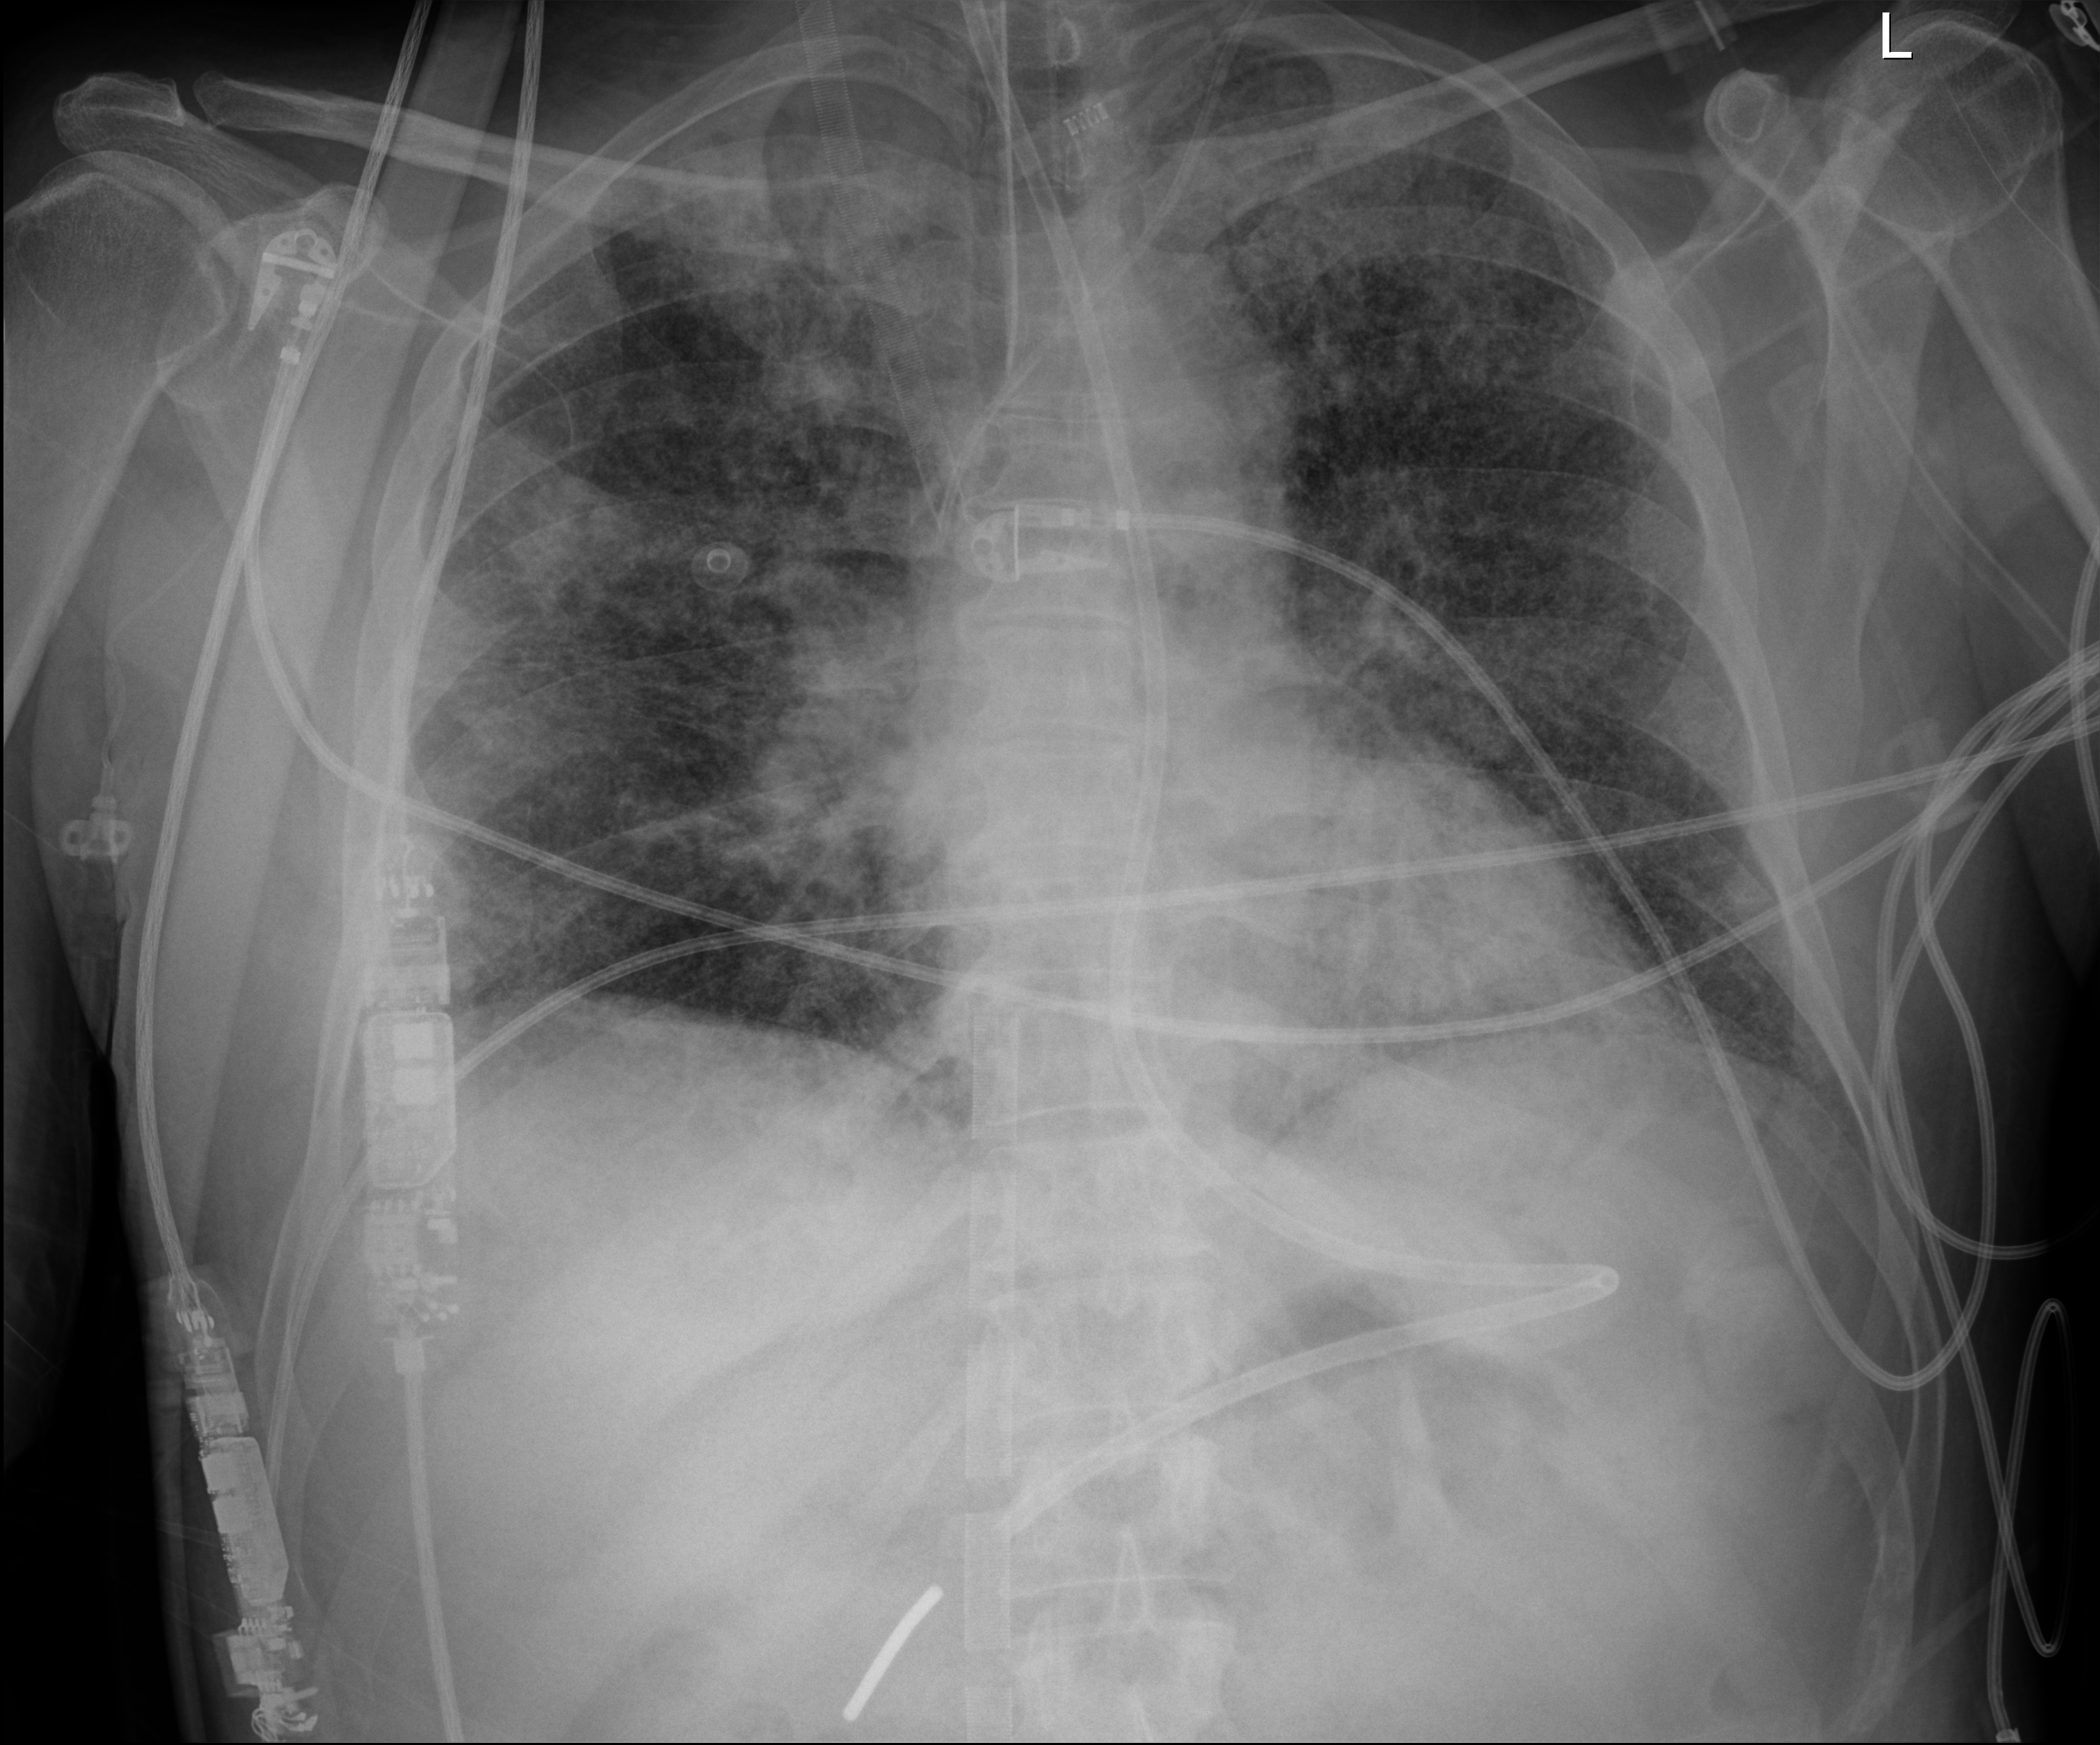
Chest radiograph, anteroposterior (AP) projection. Patient hospitalised with COVID-19; male, aged 18–59 years.
Admission-level facts for this patient (not findings on this image; timing relative to this image not recorded):
- admitted to intensive care during this hospital stay: yes